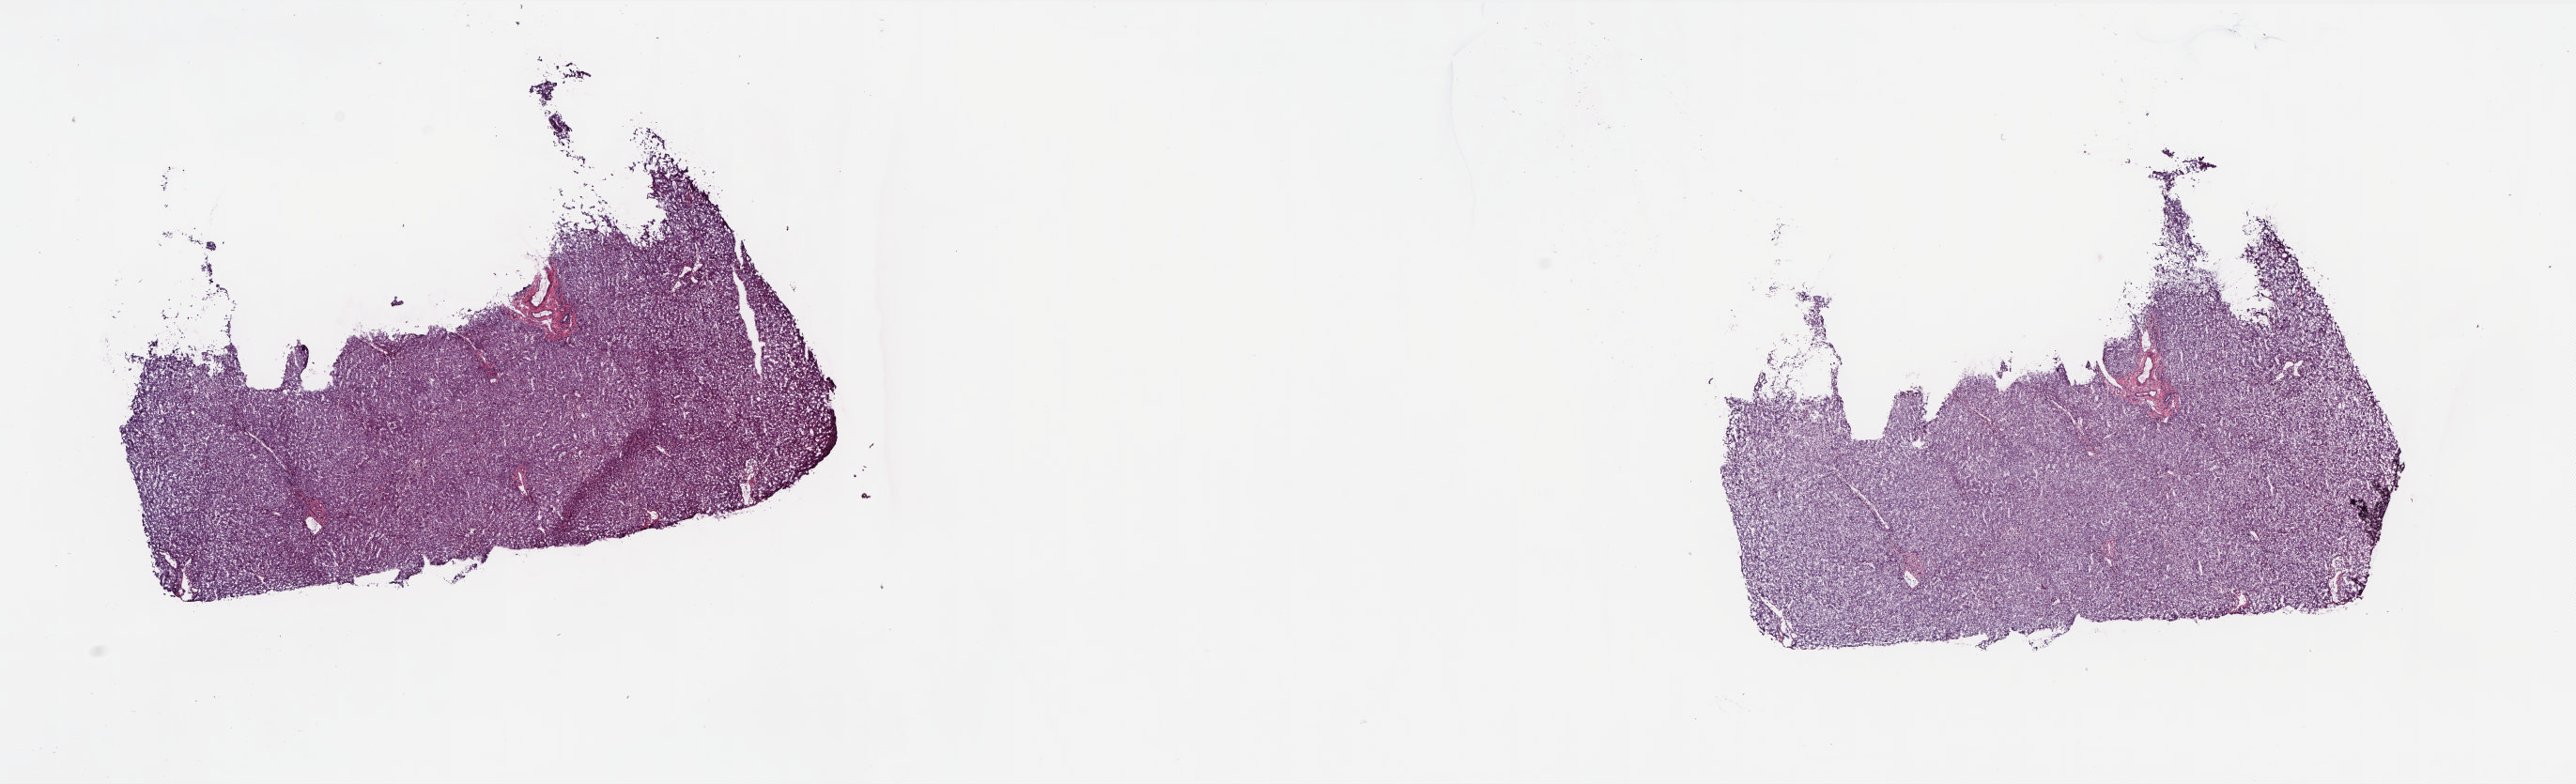
Hematoxylin and eosin (H&E) stained whole-slide image — low-resolution overview of the scanned area, about 22.1 x 6.7 mm (acquisition: 20x scan), frozen section from the top of the tissue portion, sample: solid tissue normal (non-tumour tissue), liver. Female, age 67 years at initial diagnosis. Slide review estimates, as recorded: tumour cells 0%, tumour nuclei 0%, normal cells 95%, stromal cells 5%, necrosis 0%. Inflammatory infiltration, as recorded: lymphocyte infiltration 1%, monocyte infiltration 0%, neutrophil infiltration 0%.
This section: solid tissue normal (non-tumour) sample from the same patient. Patient diagnosis: Hepatocellular carcinoma, NOS.